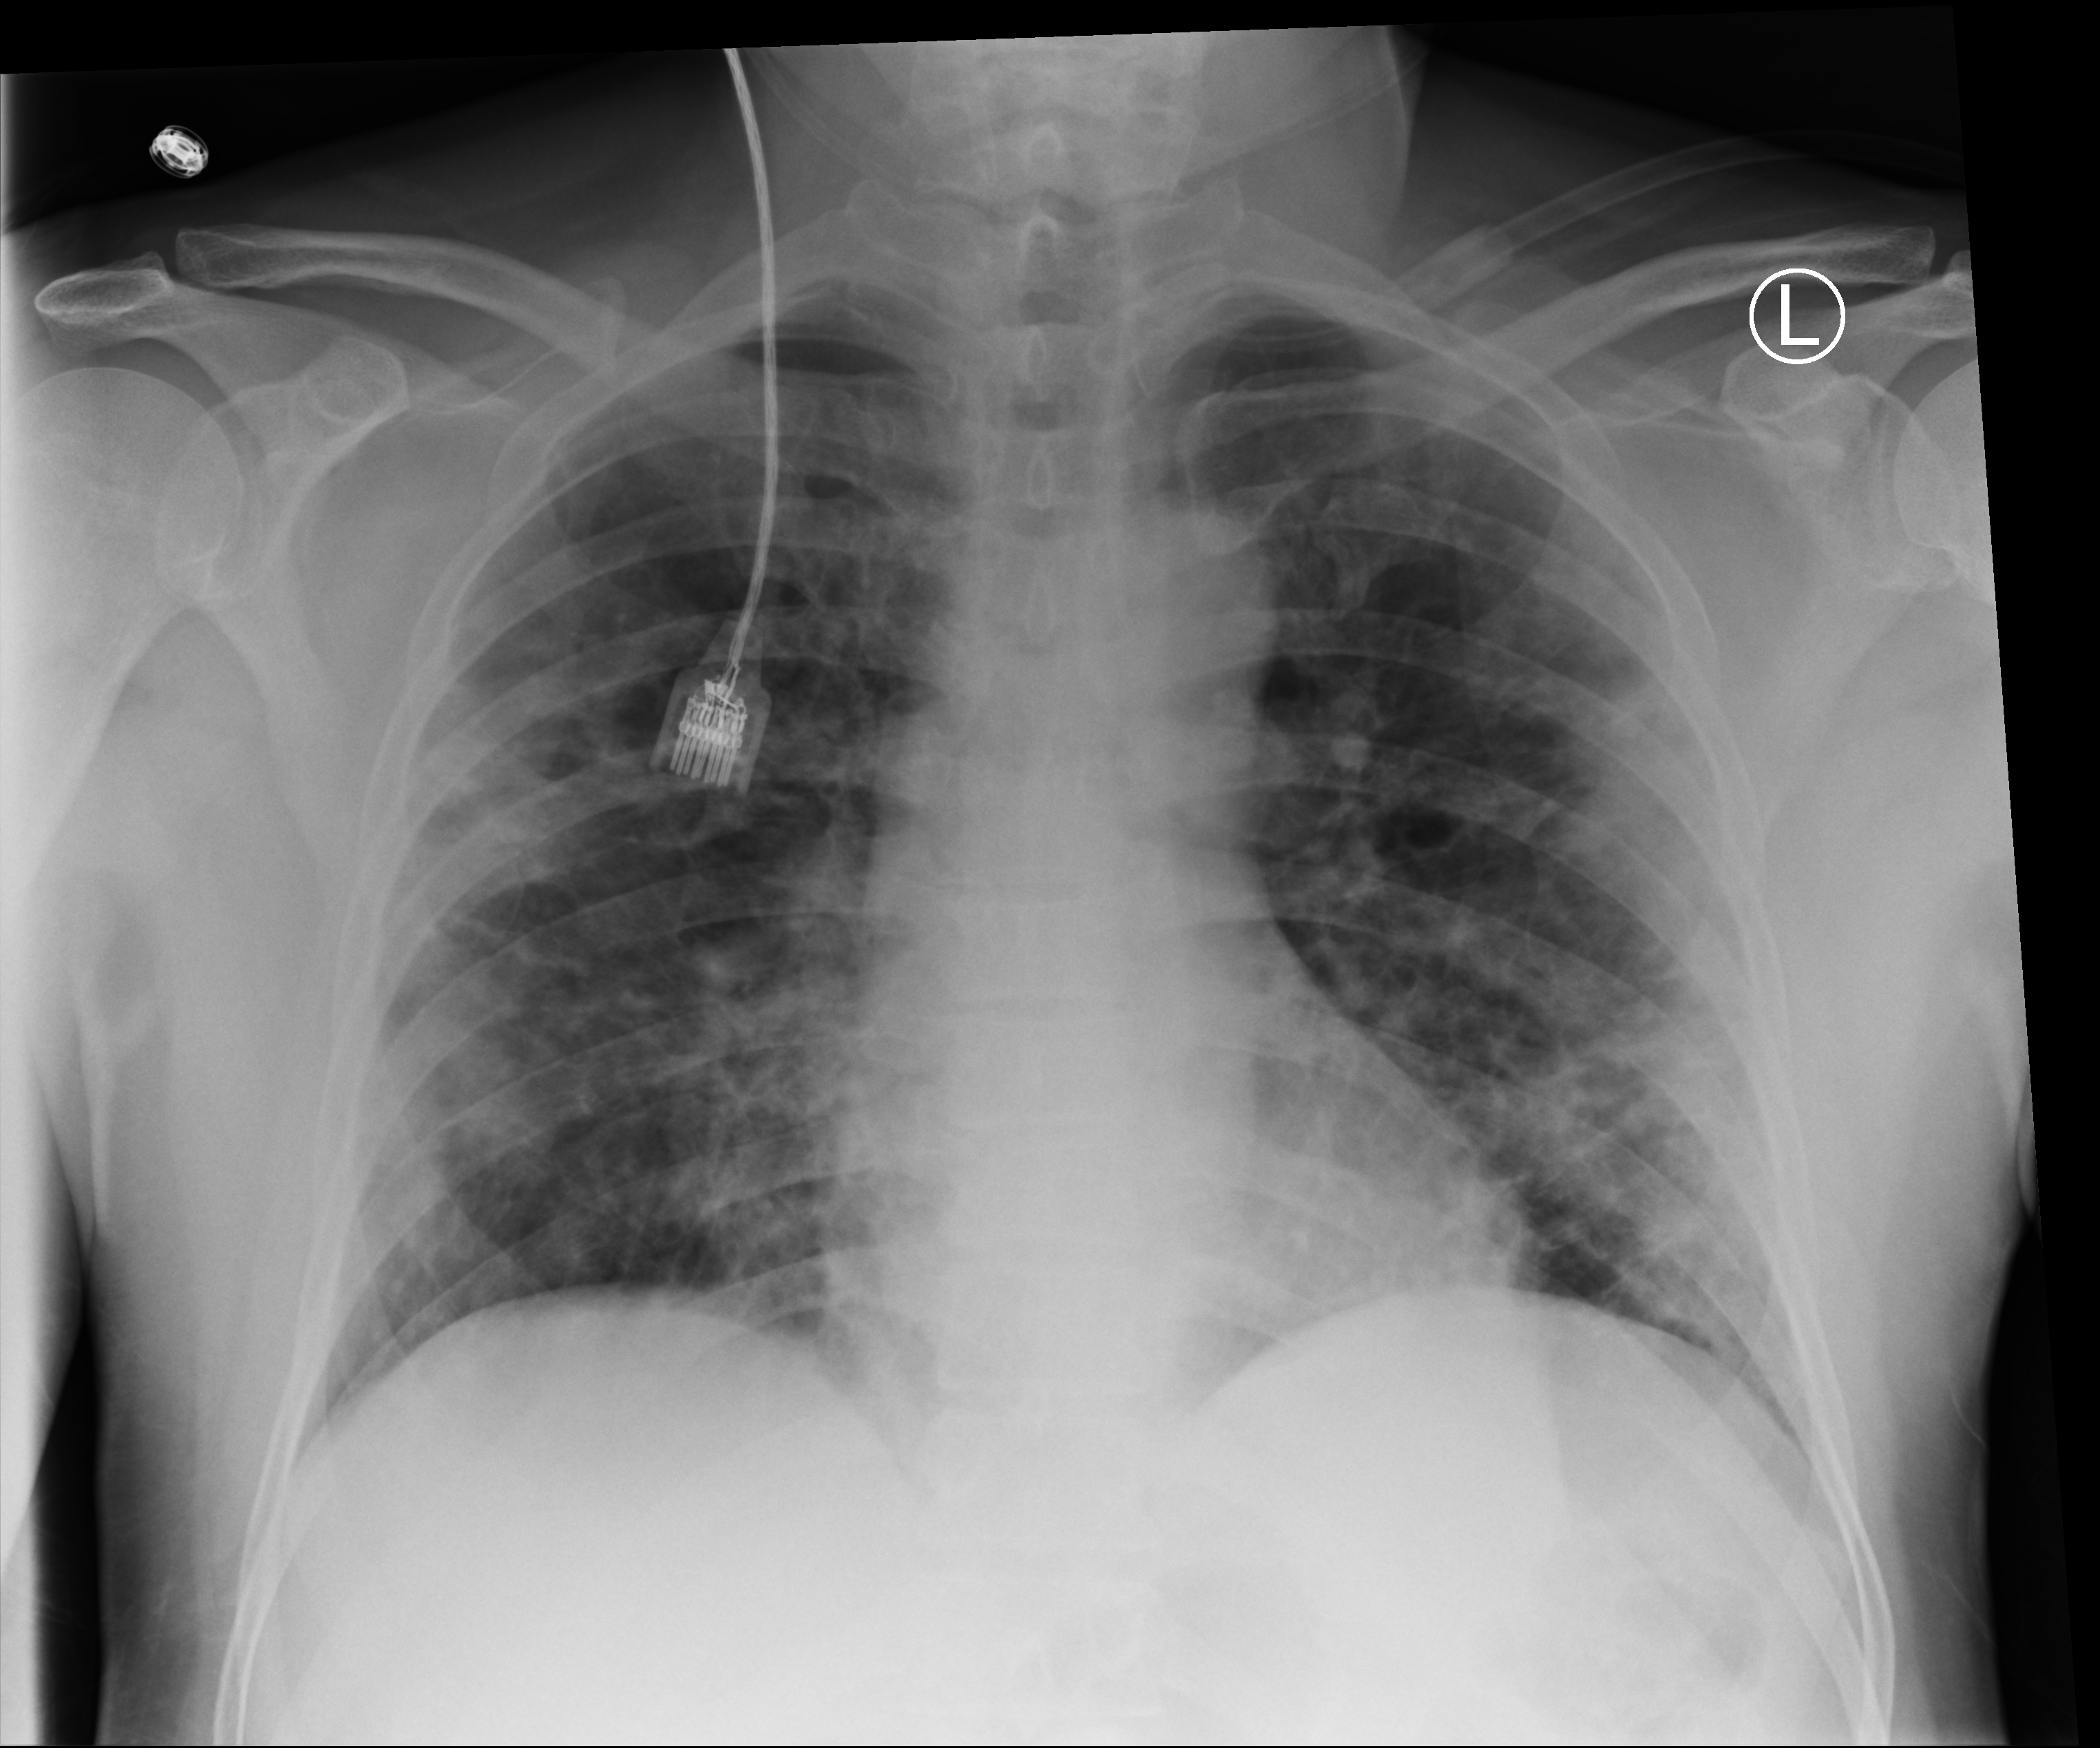
Chest X-ray (portable); anteroposterior (AP) projection. Male patient hospitalised with COVID-19, age 18–59 years.
Admission-level facts for this patient (not findings on this image; timing relative to this image not recorded): hypertension (admission record): no; mechanically ventilated during this hospital stay: no.